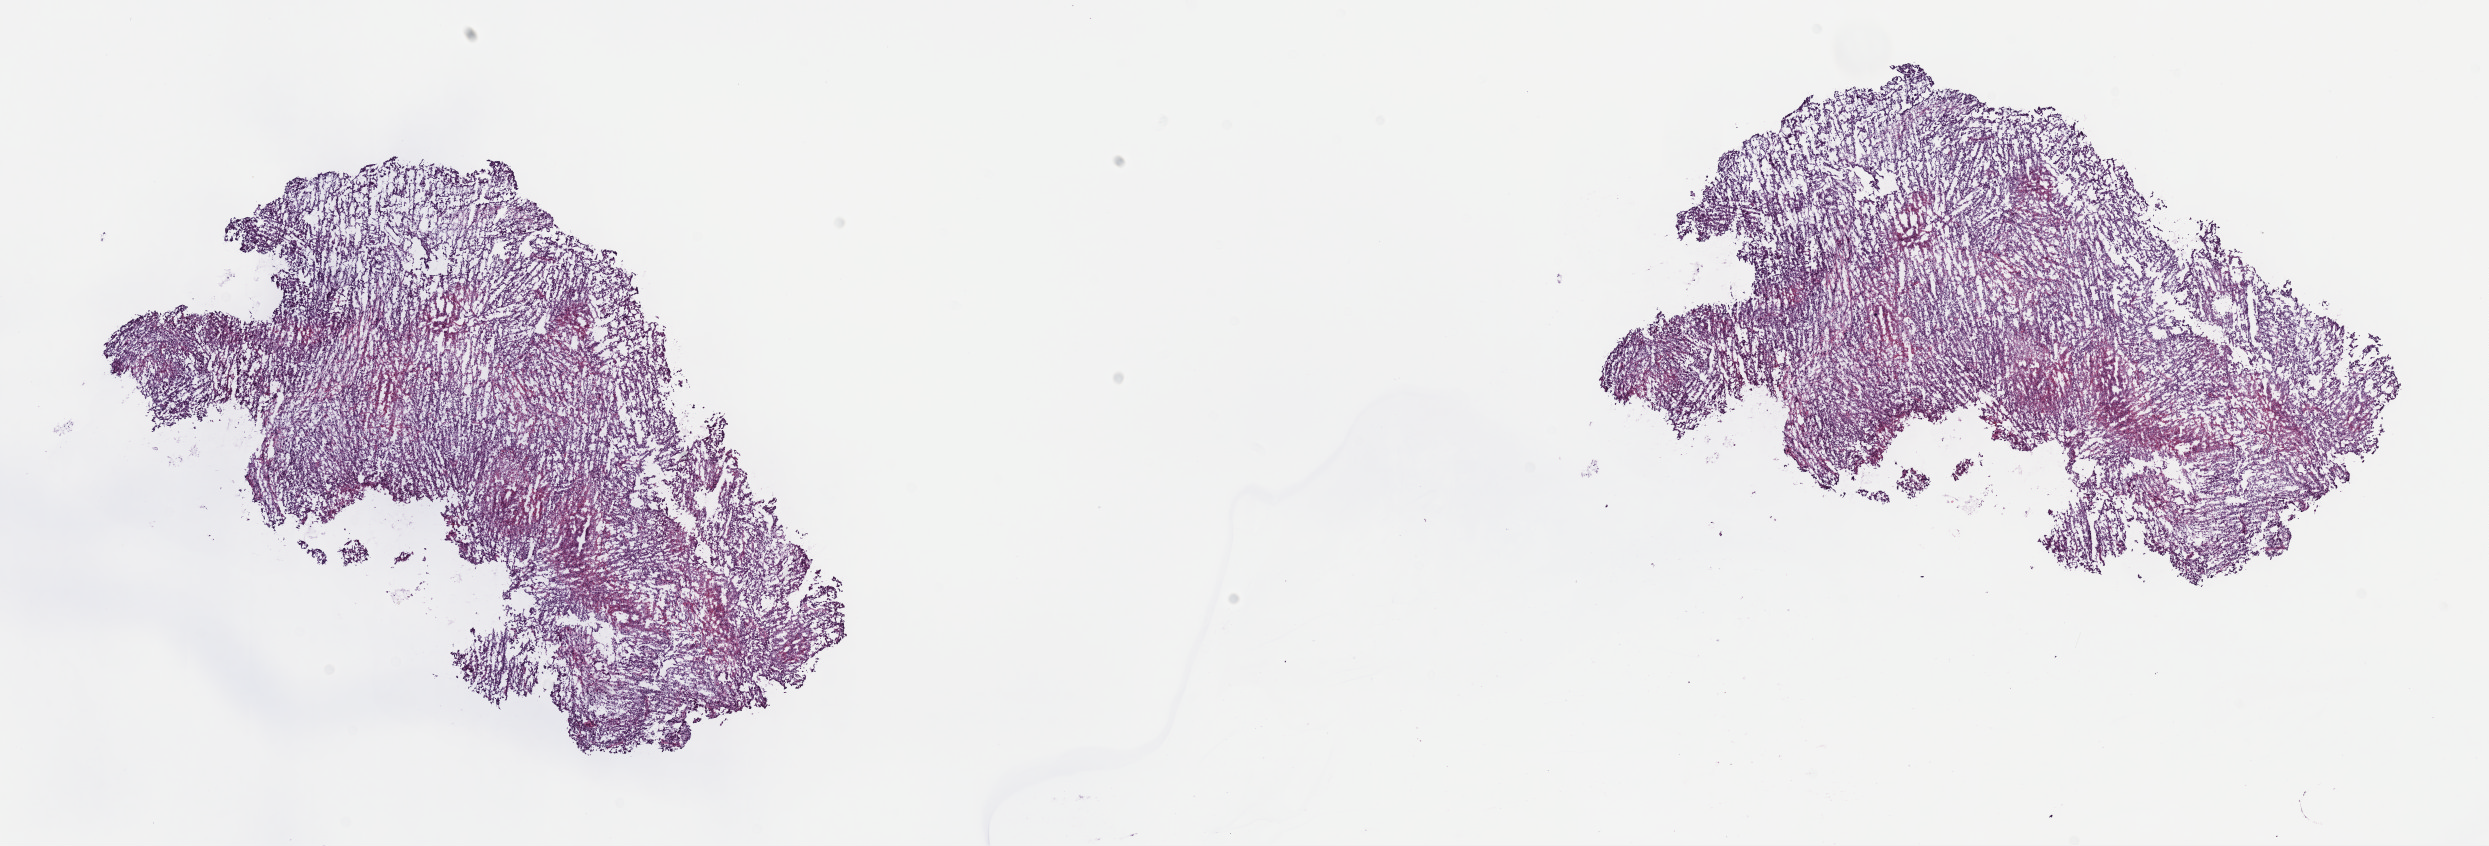
Whole-slide histology image, Hematoxylin and eosin (H&E) stained — a low-resolution overview of the entire scanned area, about 20.1 x 6.8 mm (acquisition: 40x scan). Frozen section from the top of the tissue portion. Mesothelium, primary tumour sample. Patient: male, age at initial diagnosis 65 years. Pathologist review of this section (percent, as recorded): tumour cells 83%, tumour nuclei 70%, normal cells 0%, stromal cells 0%, necrosis 17%. Inflammatory infiltration, as recorded: lymphocyte infiltration 2%, monocyte infiltration 0%, neutrophil infiltration 0%.
• histologic diagnosis: Mesothelioma, malignant (pleura, NOS)
• AJCC pathologic stage: III (6th edition)